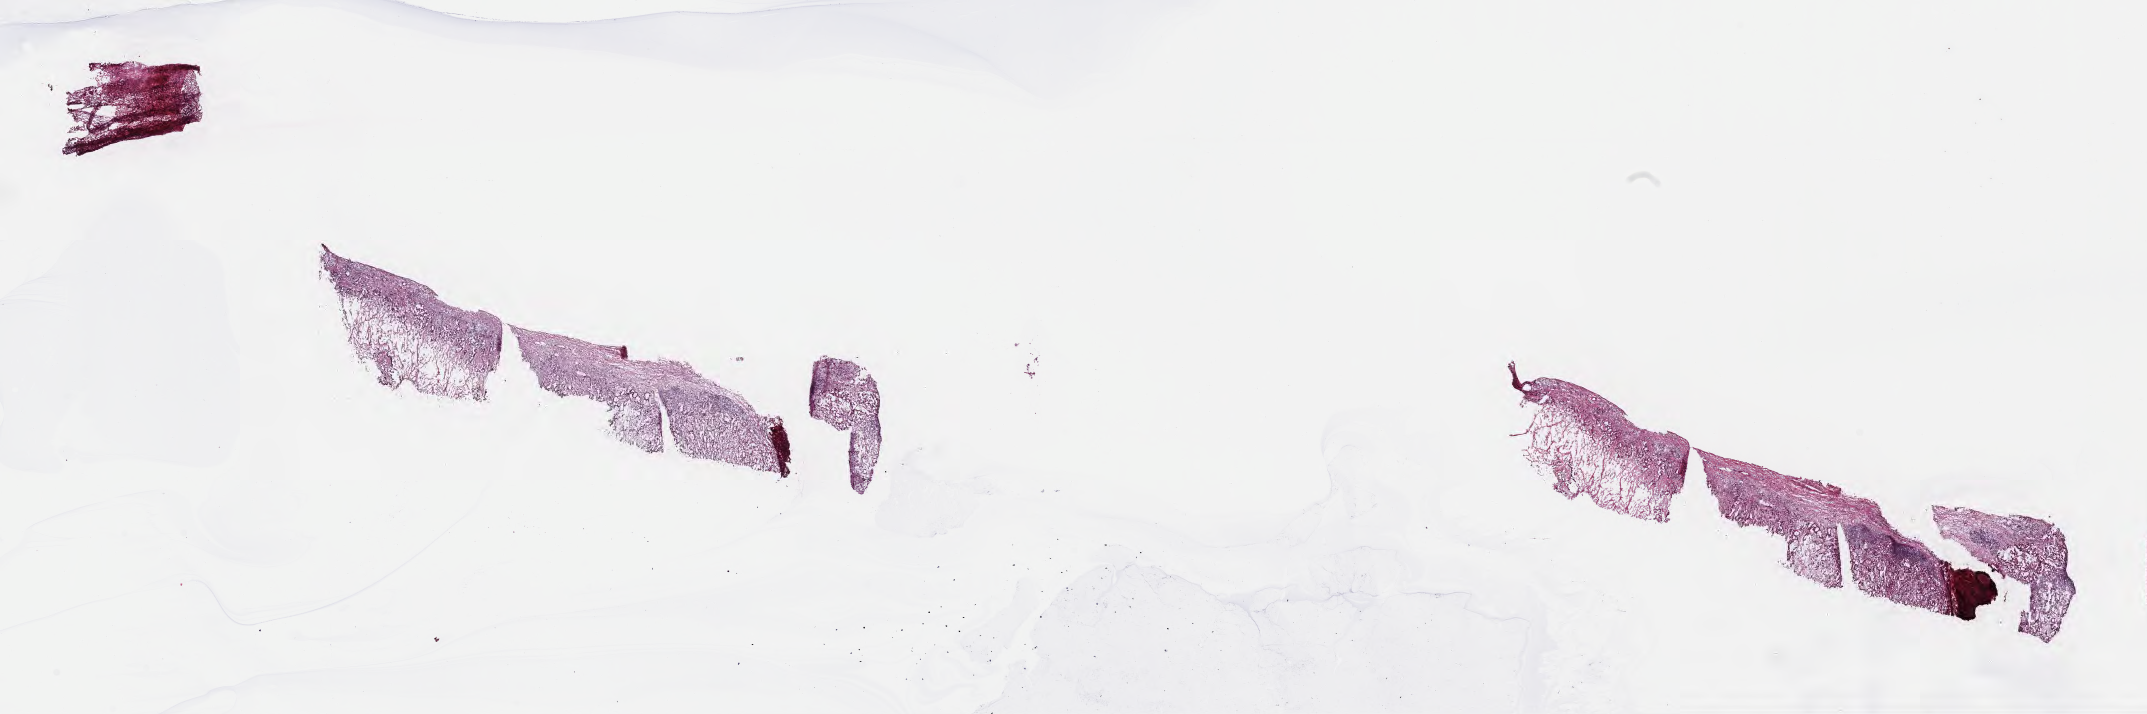
Whole-slide image, hematoxylin and eosin (H&E) stain, shown as a low-resolution overview of the whole scanned area (about 34.7 x 11.6 mm); frozen section; metastatic tumor tissue, resected from intra-abdominal lymph nodes. Patient: female, age at initial diagnosis 75 years. Pathologist review of this section (percent, as recorded): tumor cells 30%, tumor nuclei 40%, stromal cells 70%, necrosis 0%, normal cells 0%. Inflammatory infiltration, as recorded: lymphocyte infiltration 0%, monocyte infiltration 0%, neutrophil infiltration 0%.
Section: bottom of the tissue portion. Patient diagnosis (primary): Adenocarcinoma, metastatic, NOS.